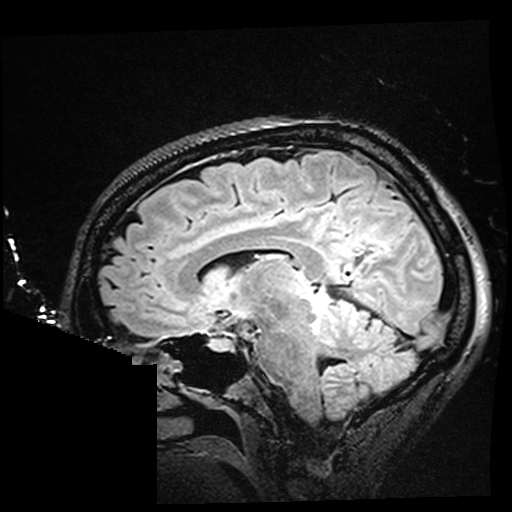
Brain MRI from a brain-tumour surgery series, one sagittal slice. Position 98 of 176 along the scan axis. T2 FLAIR. 1 mm slice thickness. 512 × 512 image matrix, field of view 250 × 250 mm. From the clinical record (not read from this slice): histopathology: Oligodendroglioma; WHO grade: 2; IDH mutation: yes; tumour location: Right Parietal.
Outlined on this slice (manually delineated by an expert):
- residual tumour: bounding box <337,281,345,289> (left, top, right, bottom; pixels)